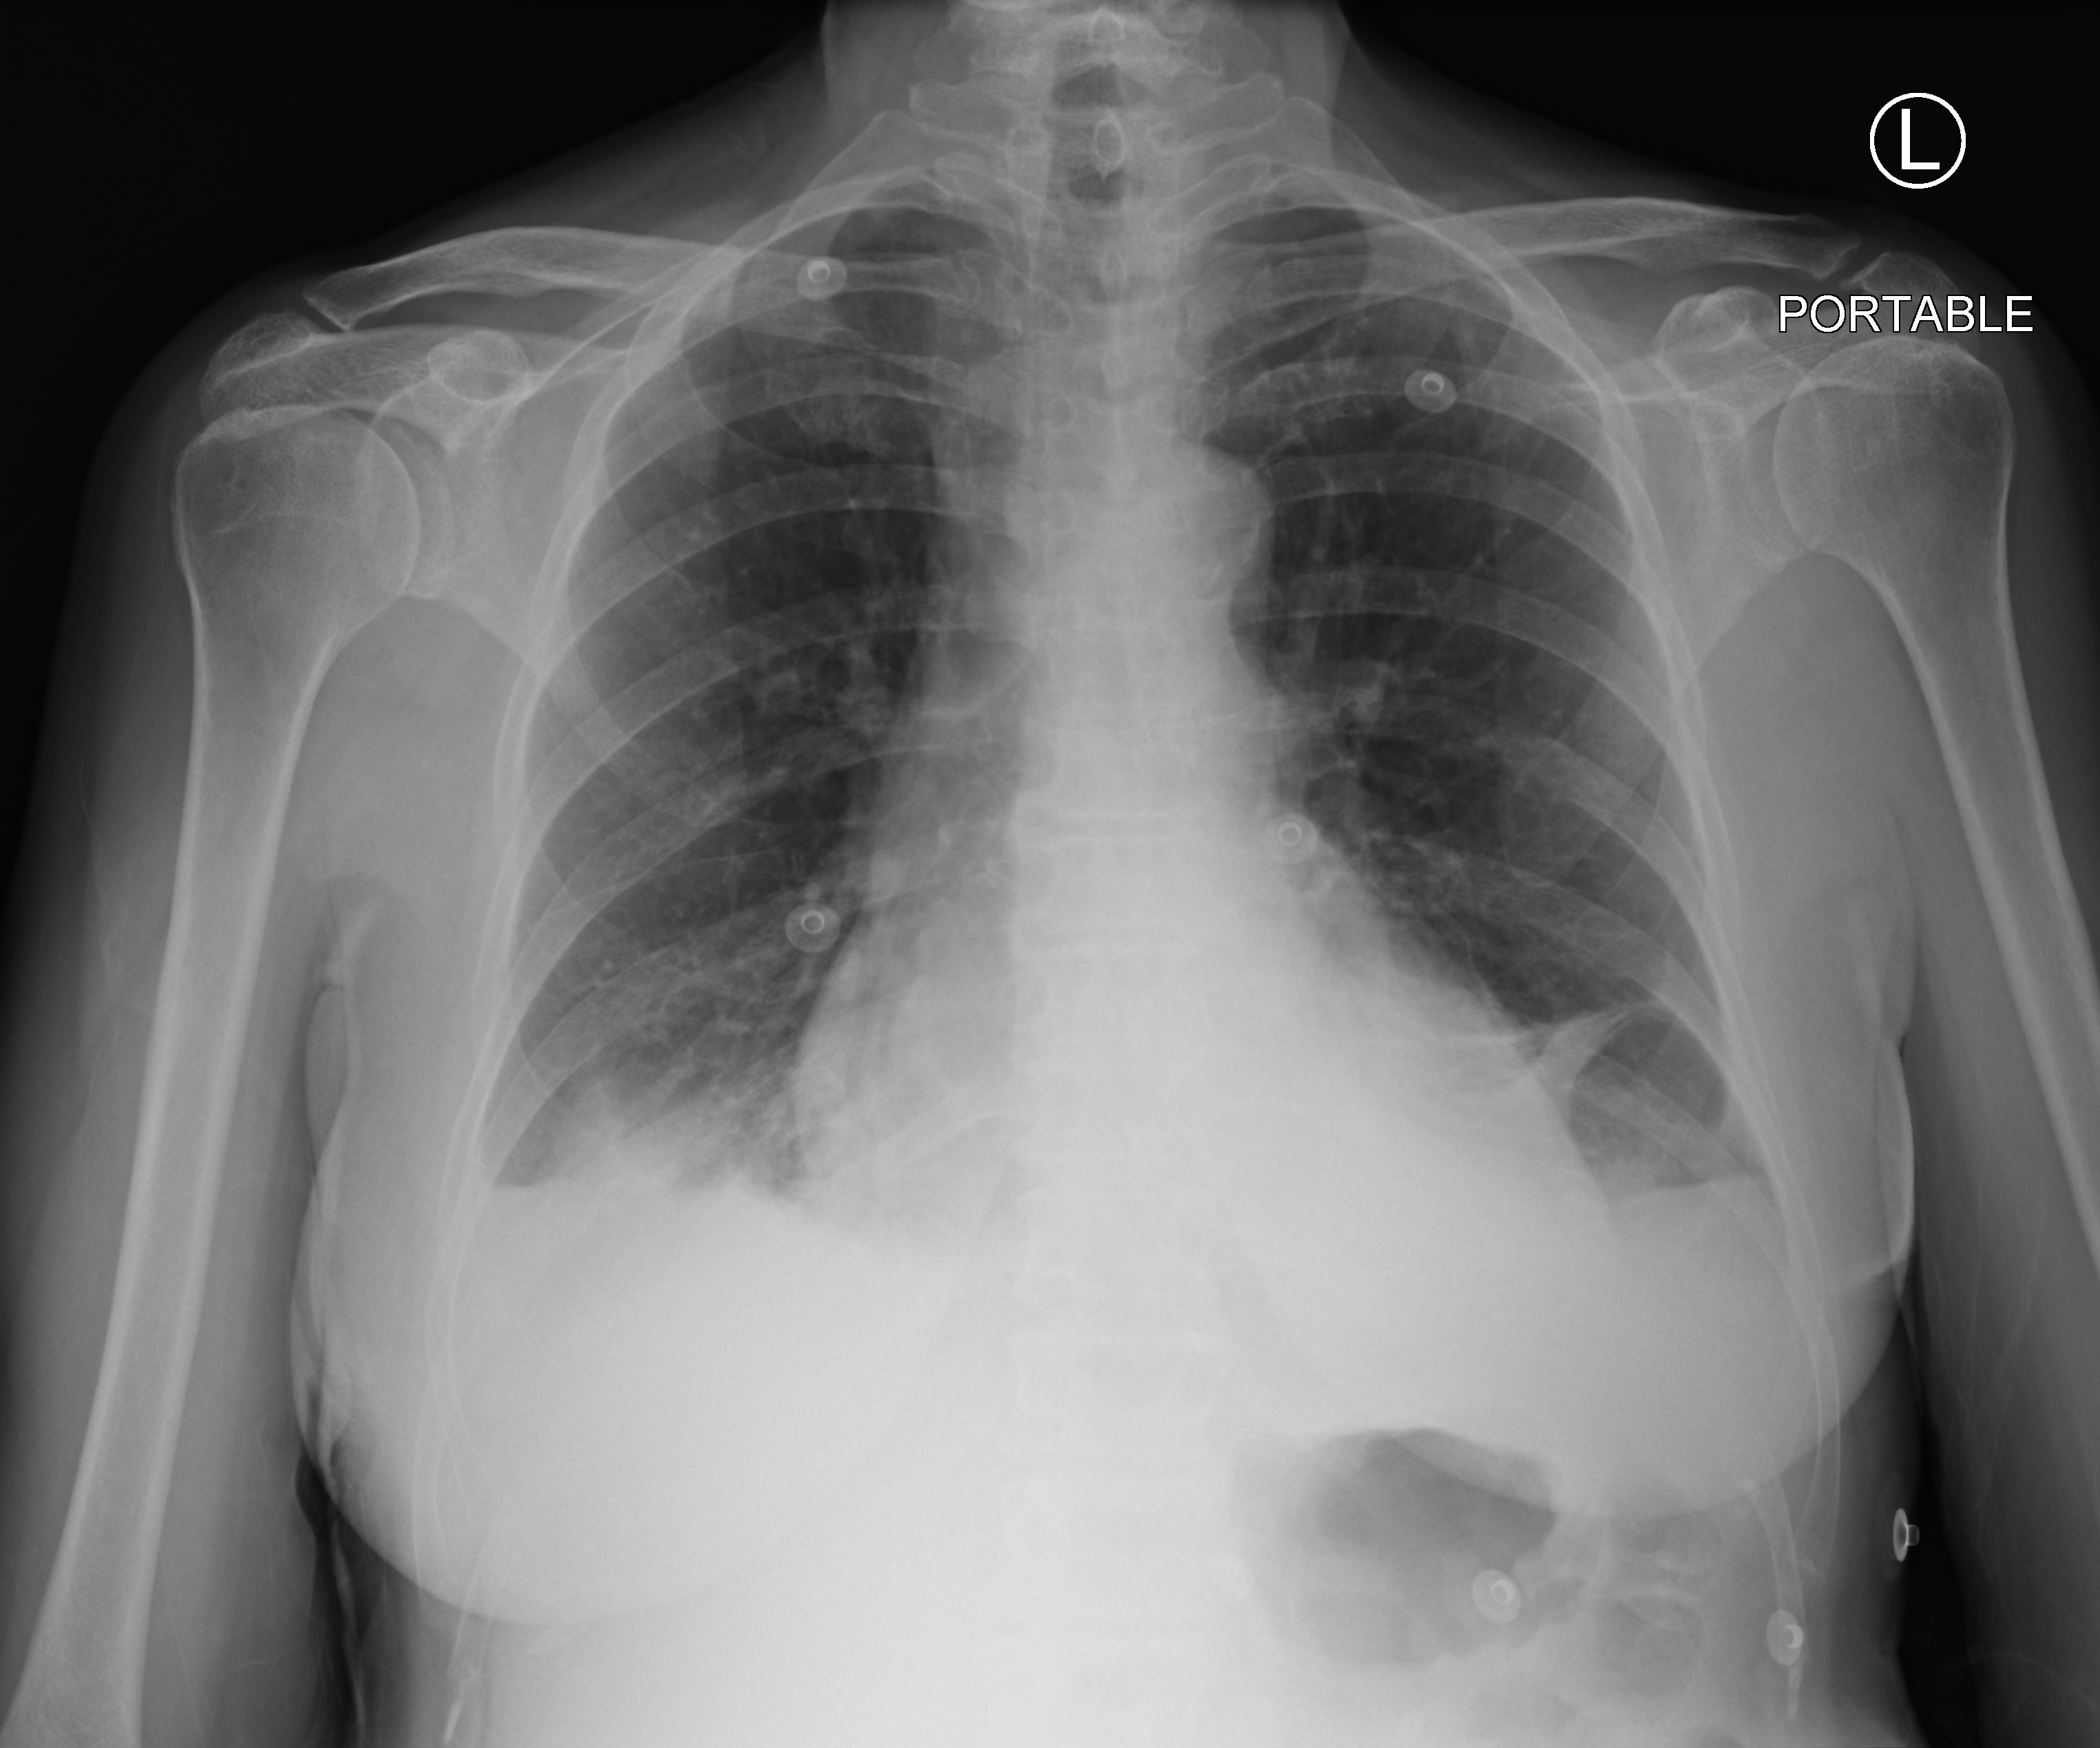
Portable chest radiograph, anteroposterior (AP) projection. Patient hospitalised with COVID-19; female, aged 75–90 years.
From the hospital-stay record, not from the radiograph (when in the stay this image was taken is not recorded):
- mechanically ventilated during this hospital stay: no
- length of hospital stay: 3 days
- admitted to intensive care during this hospital stay: no